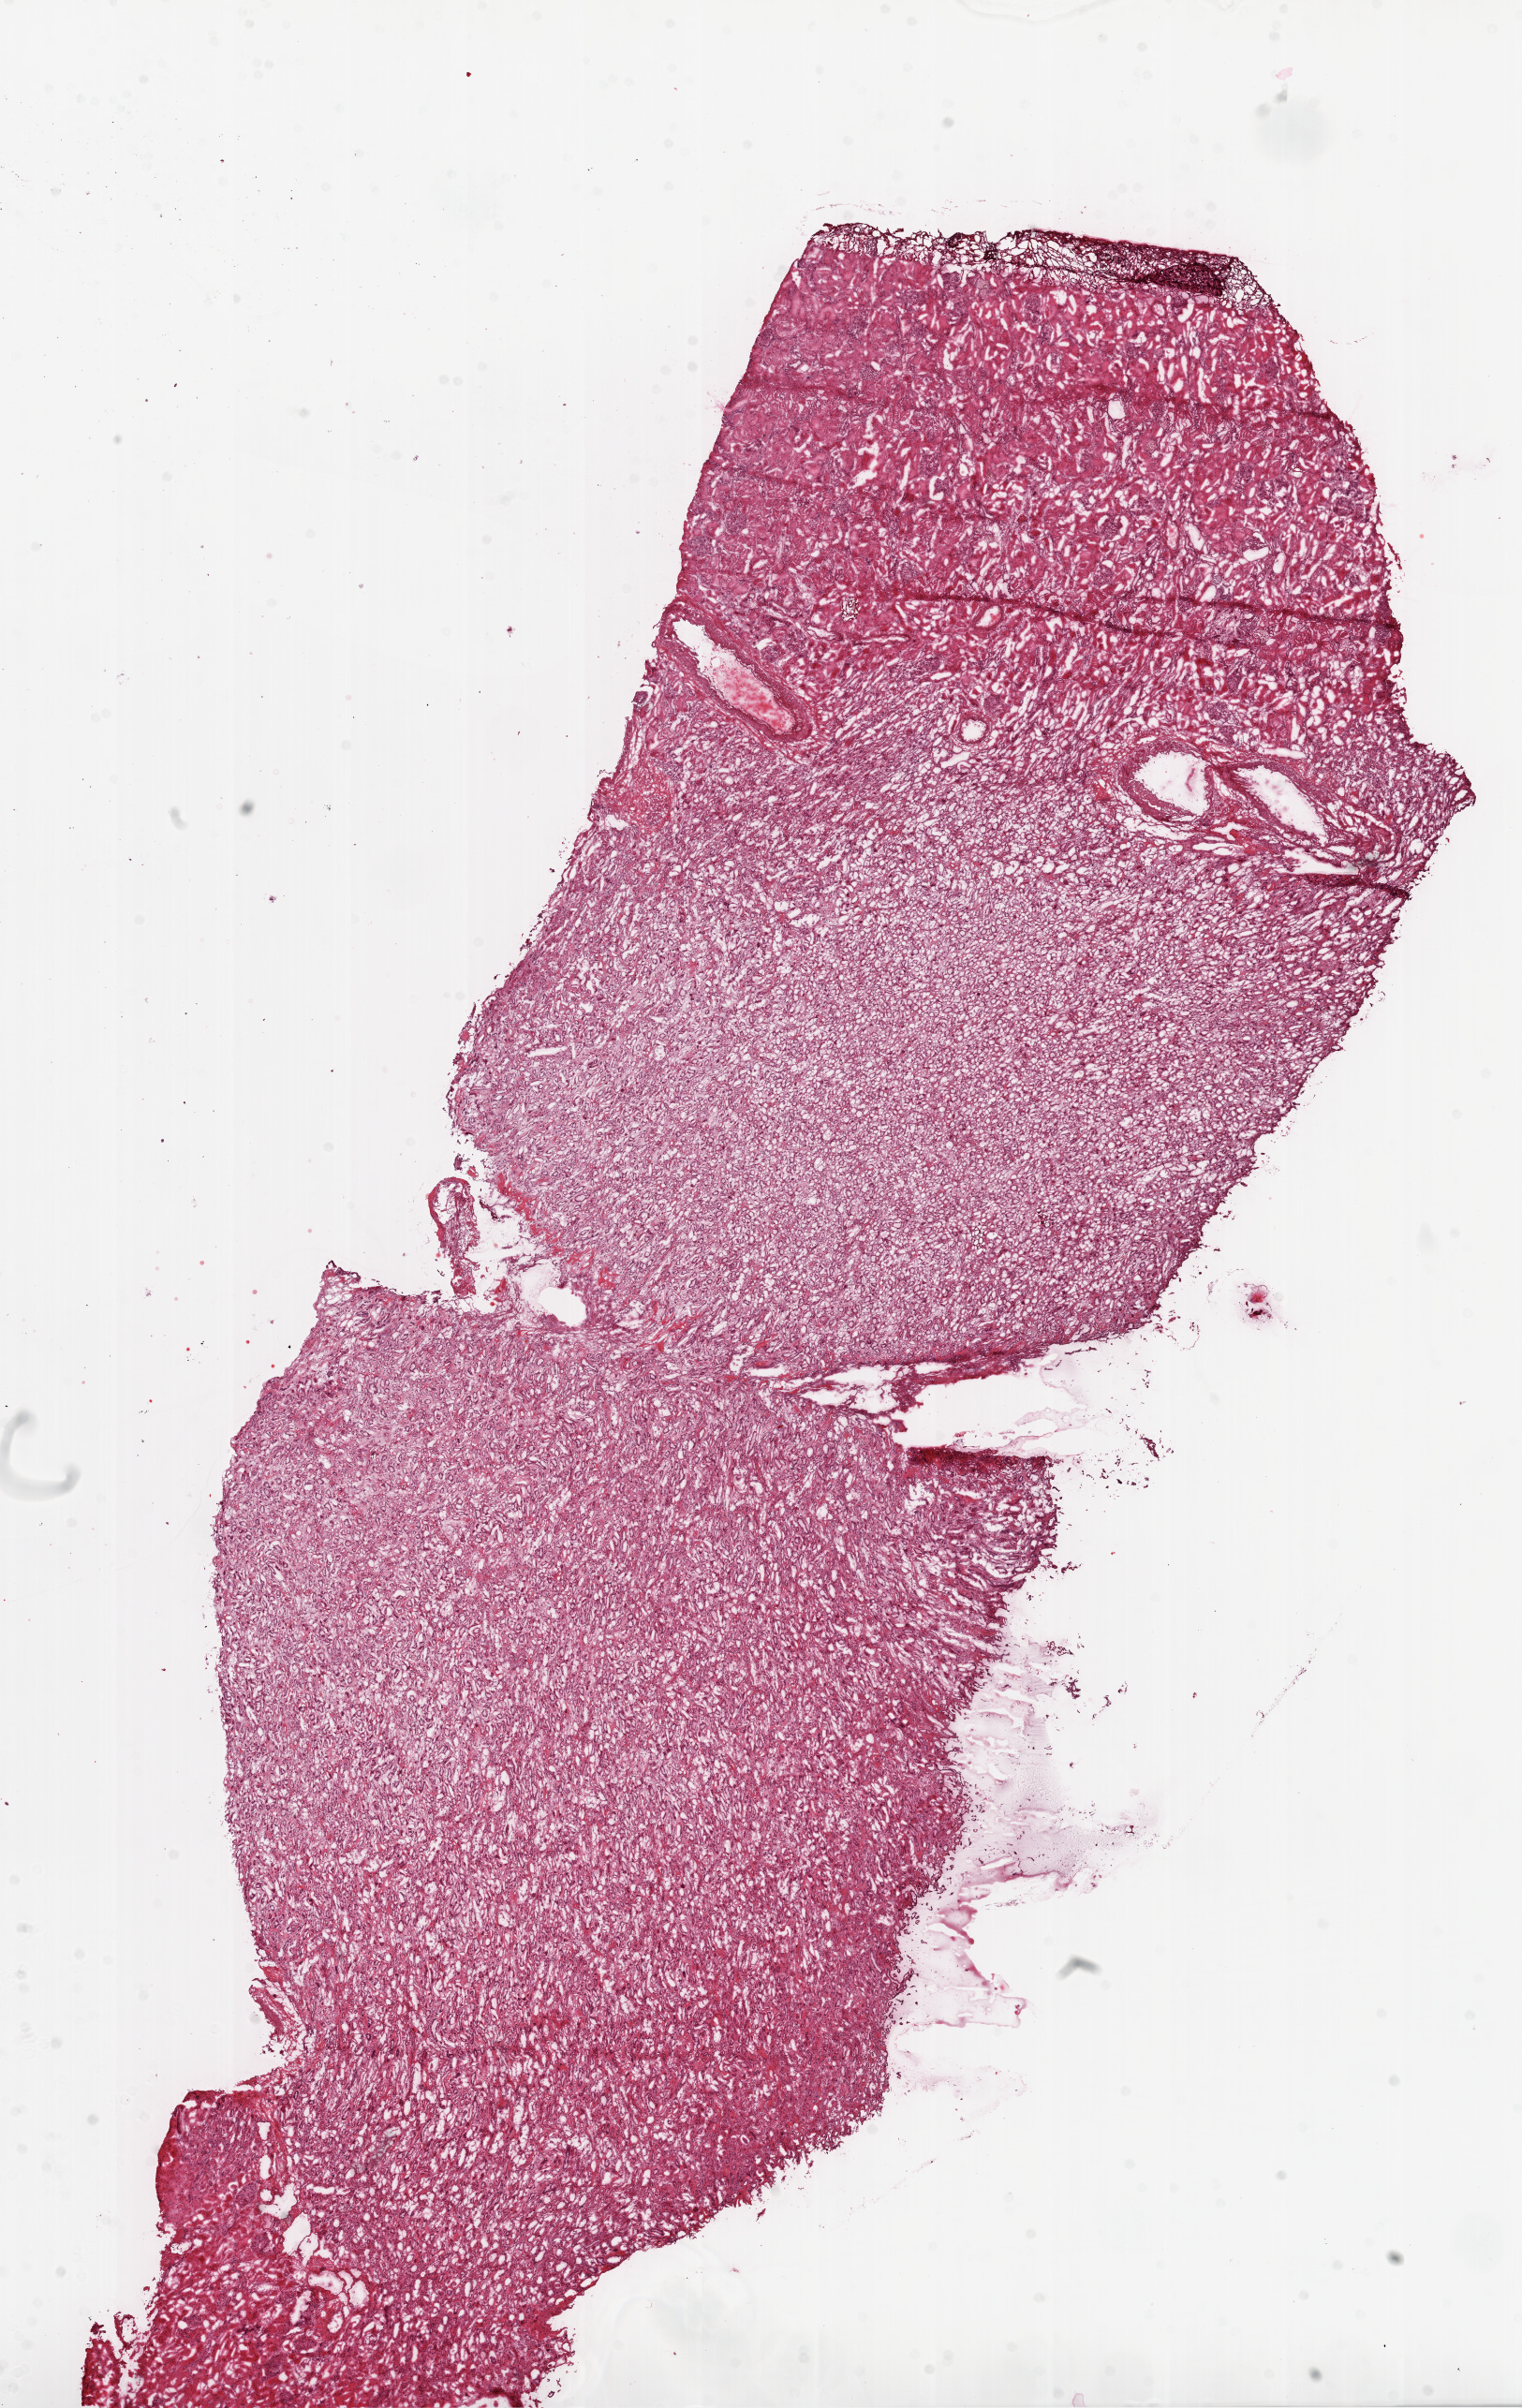
Whole-slide histology image, H&E-stained — a low-resolution overview of the entire scanned area, about 13.0 x 20.6 mm (acquisition: 20x scan). Frozen section. Kidney, solid tissue normal (non-tumour tissue) sample. Male, age 55 years at initial diagnosis.
This section: solid tissue normal sample (biorepository sample class). Patient diagnosis: Clear cell adenocarcinoma, NOS.